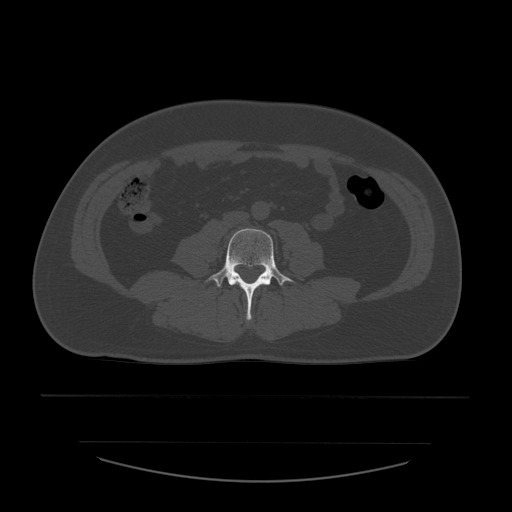
CT including the spine, one axial slice; position 149 of 532 along the scan axis; reconstruction kernel STANDARD; bone window (W 1800 / L 400 HU); 1.25 mm slice thickness; 512 × 512 image matrix, field of view 441 × 441 mm. Patient age 44 years. From the clinical record (not read from this slice): primary cancer: soft tissue sarcoma.
Outlined on this slice (semi-automatically segmented with operator editing):
- L4 vertebra: bounding box <206,229,295,320> (left, top, right, bottom; pixels)